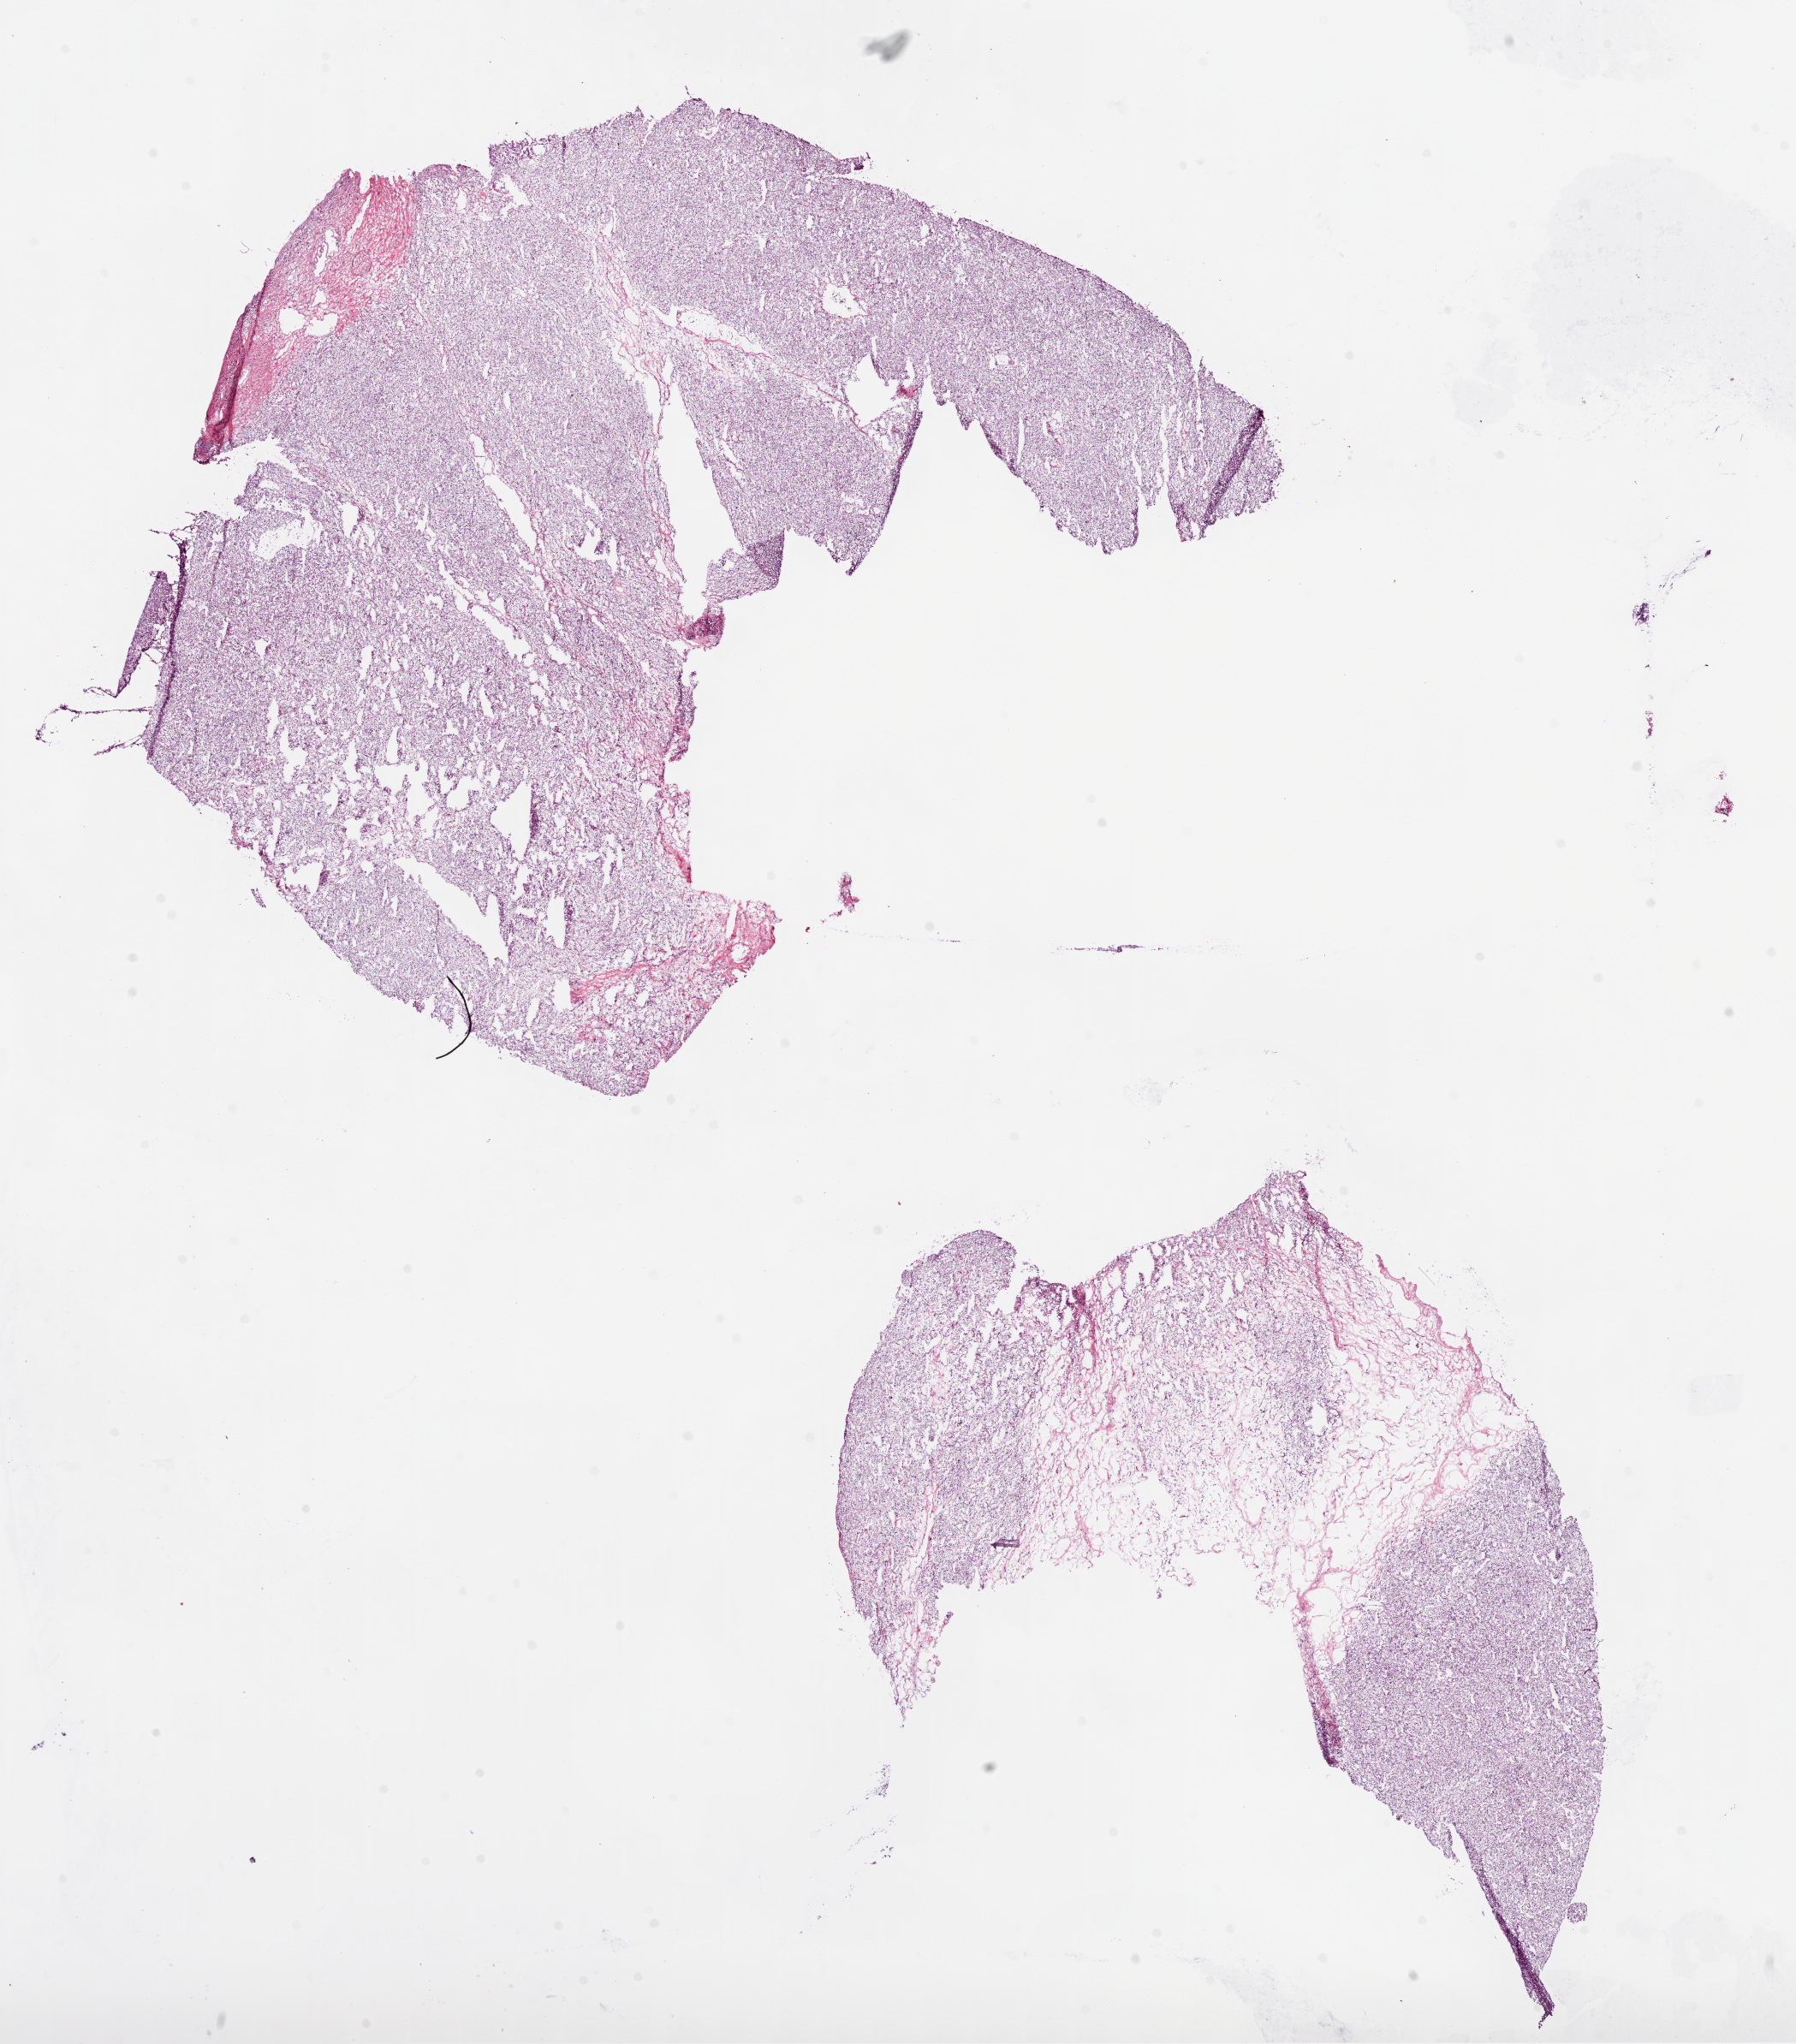
H&E whole-slide image, shown as a low-resolution overview of the whole scanned area (about 16.9 x 19.3 mm), frozen section, sample: primary tumour, kidney. Male, age 53 years at initial diagnosis. Histologic grade: G3 (poorly differentiated). Composition of this section per pathologist review: tumour cells 90%, tumour nuclei 85%, normal cells 0%, stromal cells 10%, necrosis 0%.
Laterality: right. Pathologic diagnosis: Clear cell adenocarcinoma, NOS. AJCC pathologic stage: I (6th edition).